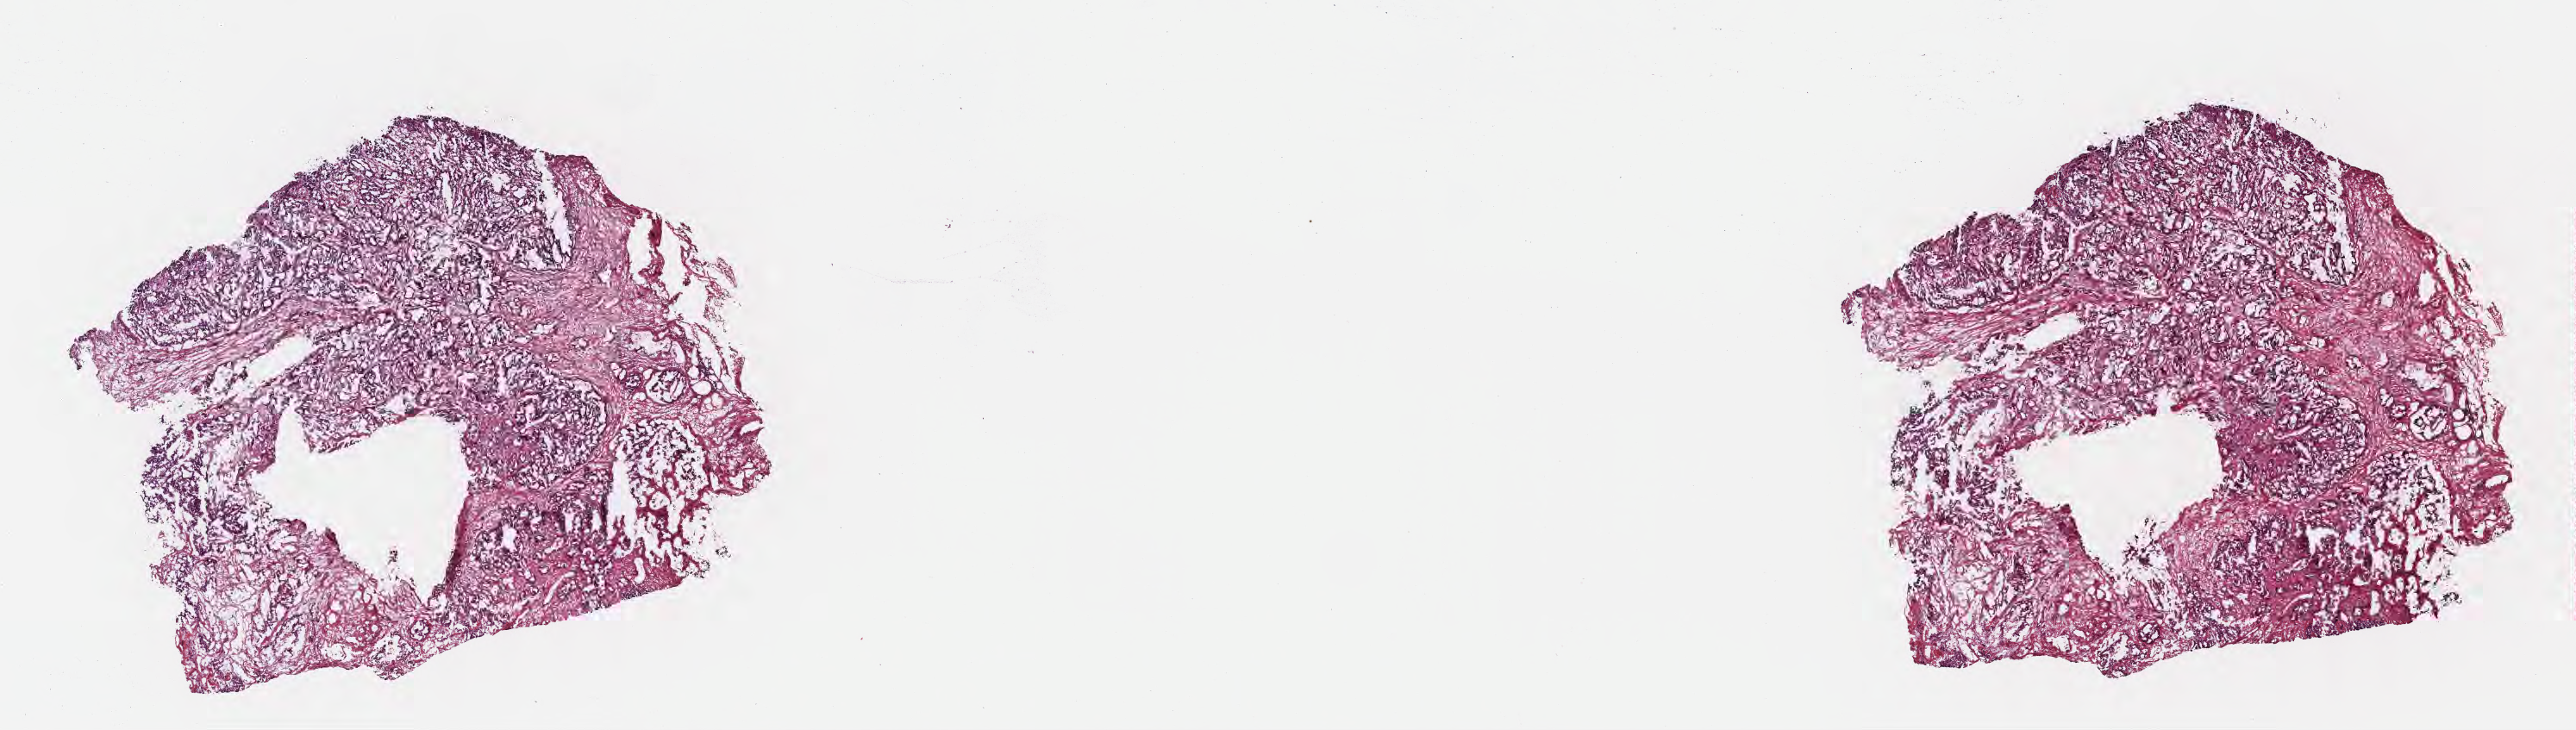
H&E whole-slide image — a low-resolution overview of the entire scanned area, about 24.1 x 6.8 mm, frozen section, specimen: metastatic tumor tissue, resected from lymph node. Male patient; age at initial diagnosis 72 years. Pathologist review of this section (percent, as recorded): tumor cells 35%, tumor nuclei 35%, stromal cells 20%, necrosis 0%, normal cells 45%. Inflammatory infiltration, as recorded: lymphocyte infiltration 7%, monocyte infiltration 1%, neutrophil infiltration 5%.
• patient diagnosis (primary): Intraductal papillary mucinous neoplasm with invasive carcinoma